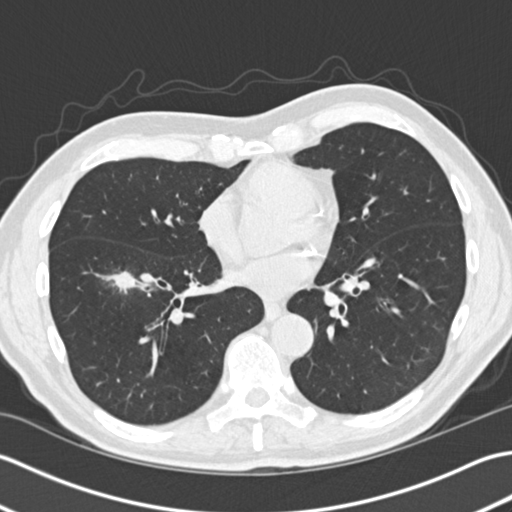
Chest CT (low-dose screening protocol), one axial image; second screening round (one year after baseline); lung window (W 1500 / L -600 HU); standard (soft-tissue) reconstruction kernel (B30f); 512 × 512 image matrix, field of view 350 × 350 mm. Male participant, aged 73 years at enrolment. Former smoker at enrolment.
- Expert reader's lesion annotation, box from (x=92, y=253) to (x=150, y=314) px.
- The exam's reader record, not a measurement of the box and not confirmed to be the same lesion: non-calcified nodule or mass ≥4 mm, right lower lobe, 18 × 15 mm, spiculated (stellate) margins, soft tissue attenuation, pre-existing on the prior screen: yes.
- Lung cancer was diagnosed 87 days after this screen: non-small cell carcinoma, right lower lobe, stage IA (AJCC 6th edition), 30 mm at pathology.